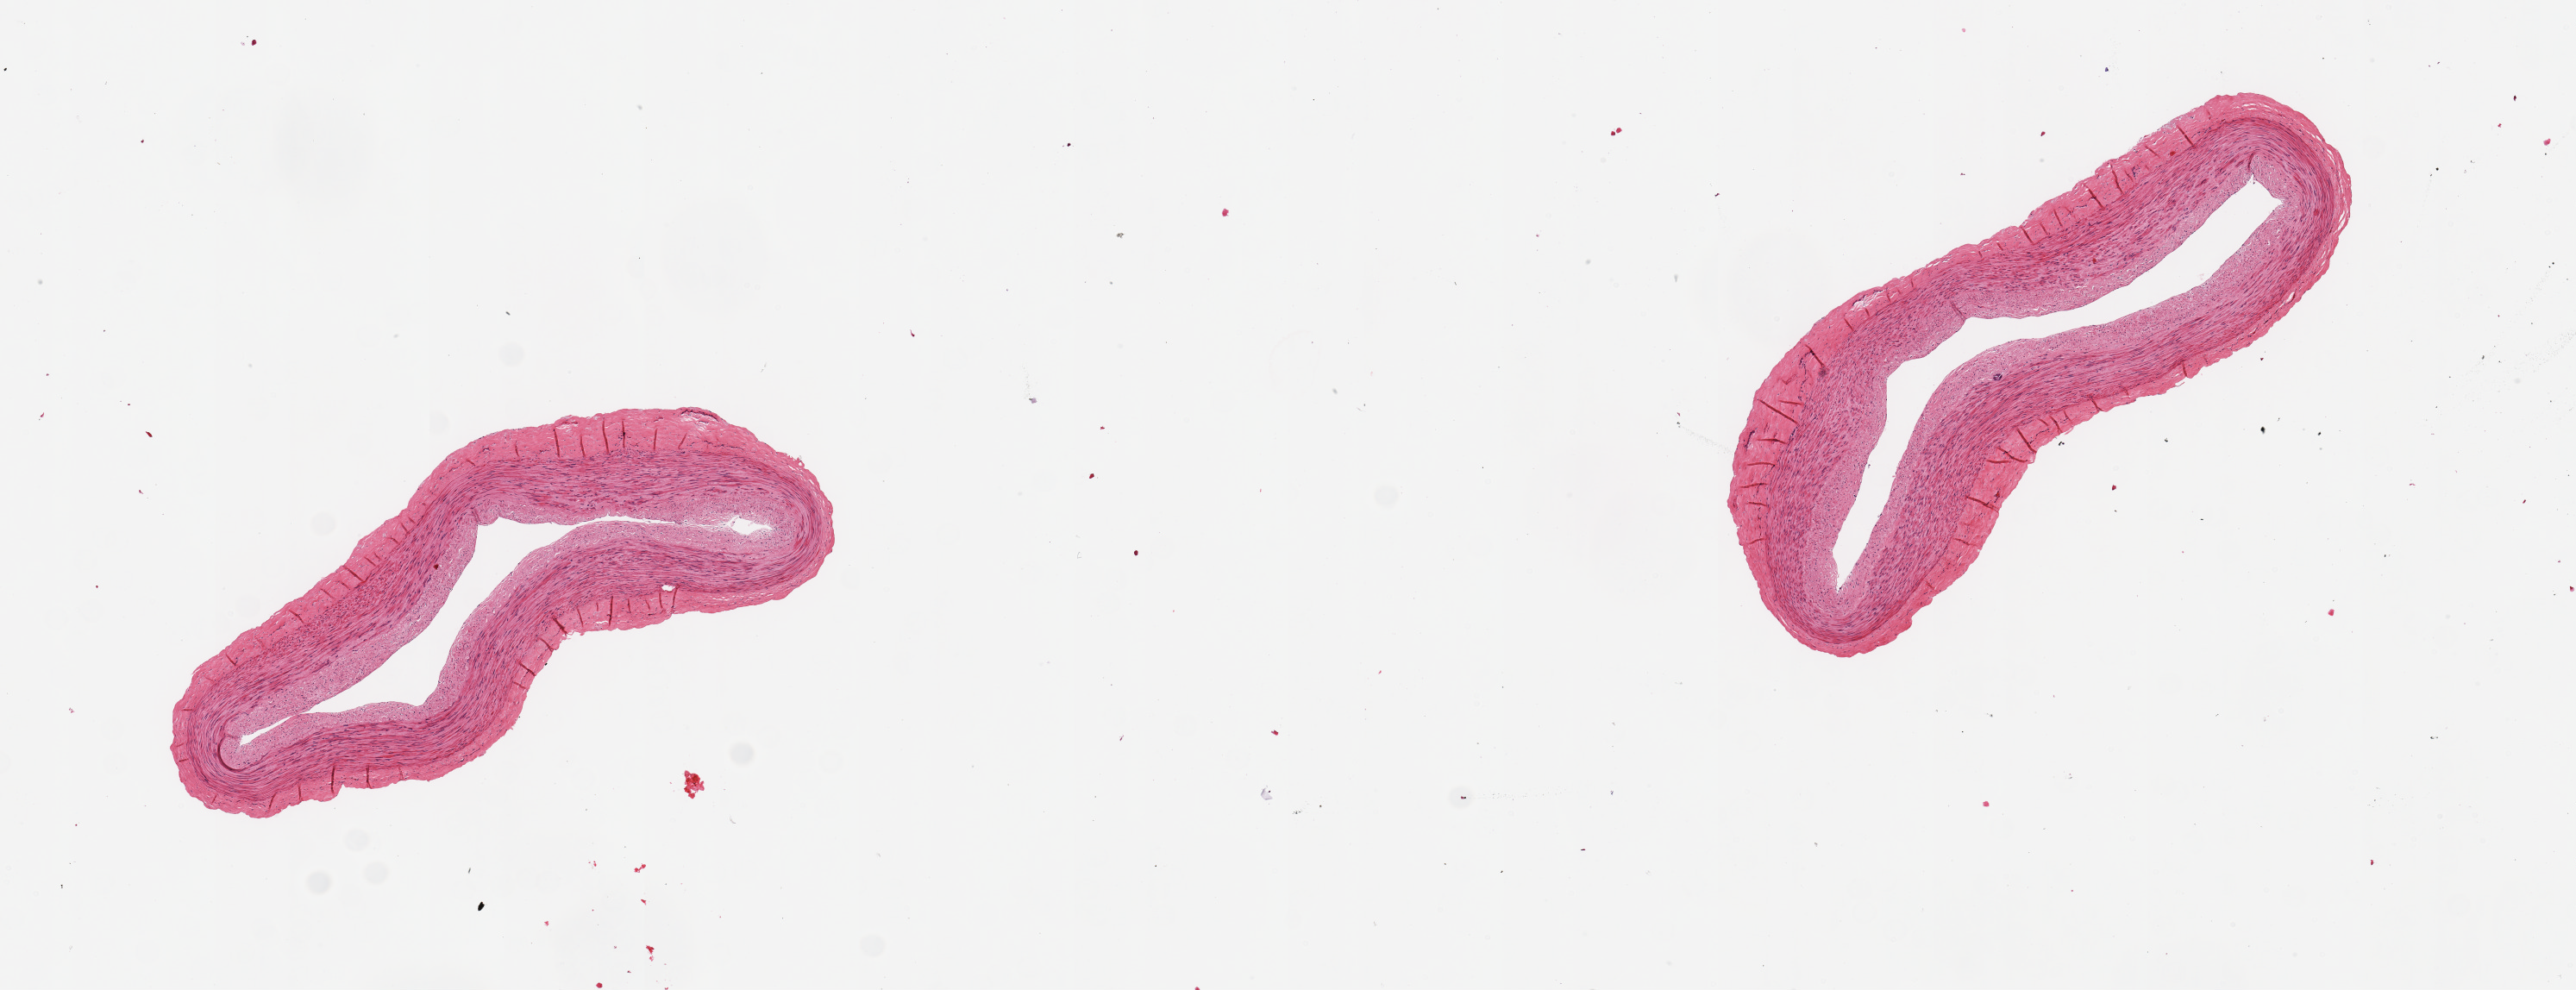
Hematoxylin and eosin (H&E) whole-slide image — a low-resolution overview of the entire scanned area, about 11.8 x 4.5 mm (from a 20x scan), PAXgene-fixed, paraffin-embedded tissue, sampled site (target tissue): tibial artery, donor tissue sample. Donor: male.
Pathologist's review note for this sample: 2 pieces ~2mm d. Good clean specimen.